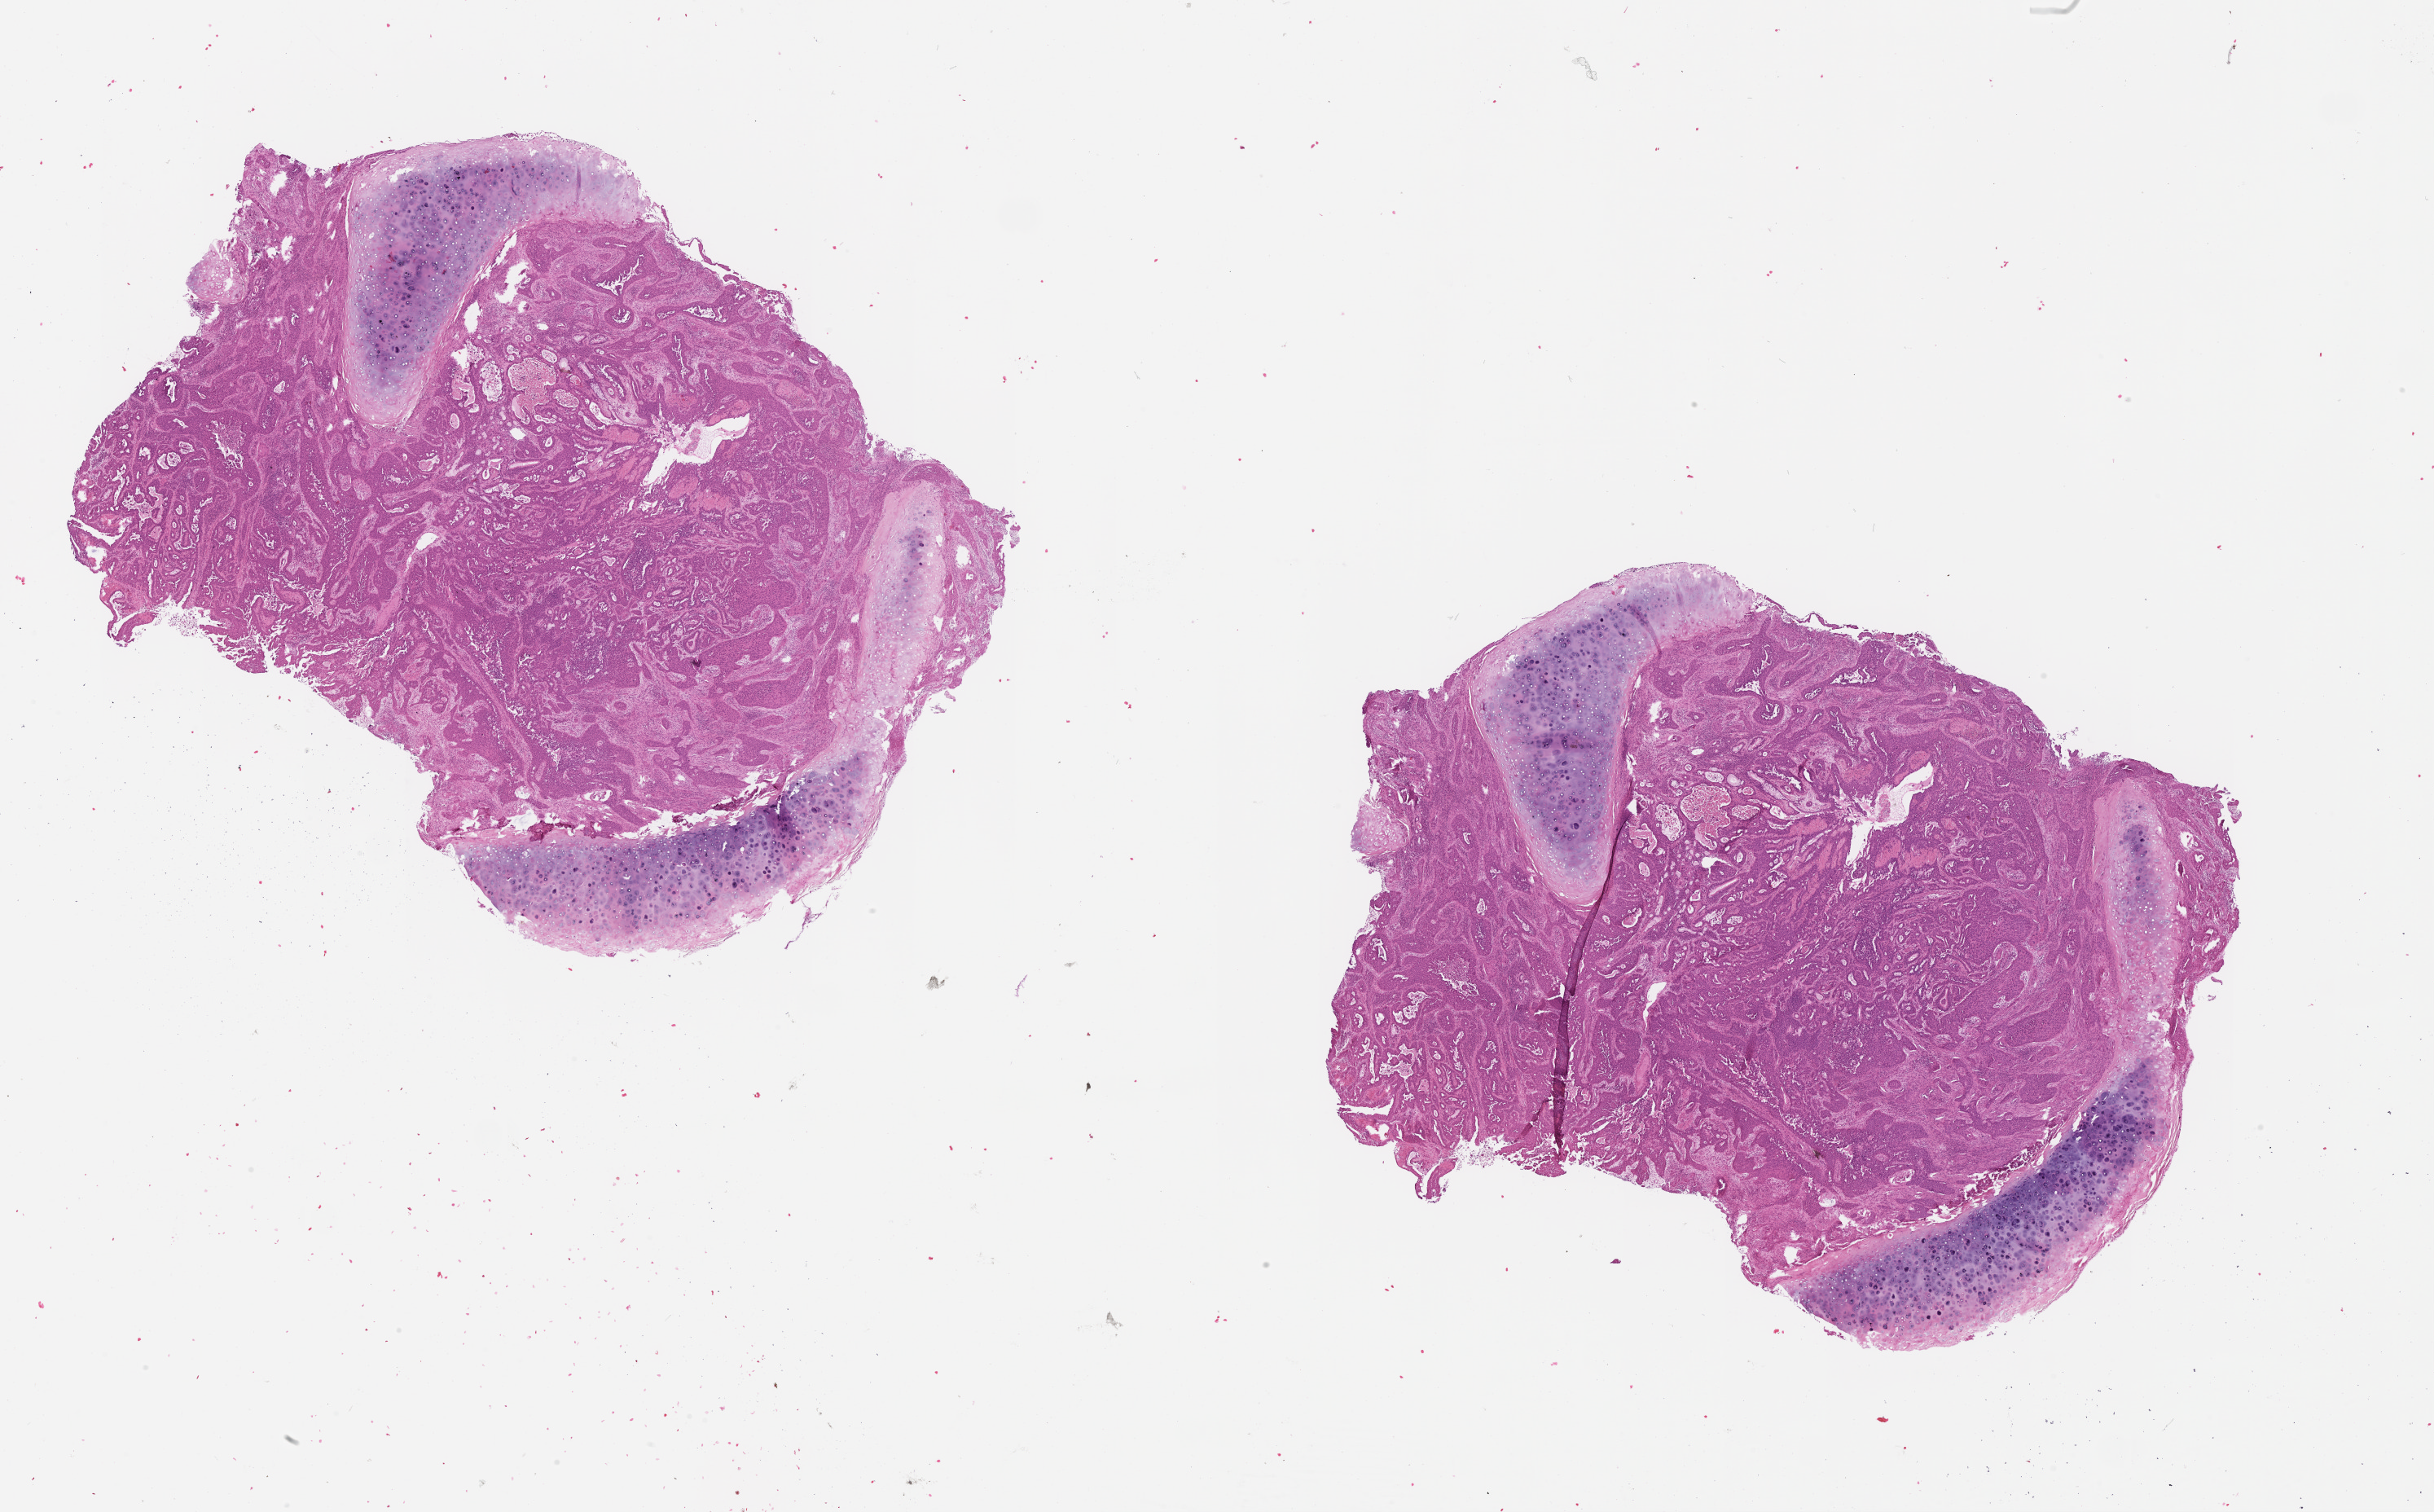
Digitized Hematoxylin and eosin (H&E) stained tissue section (whole slide) — whole scanned area (about 24.1 x 14.9 mm) shown as a low-resolution overview. Lung, tumour tissue. 55-year-old male patient.
- patient diagnosis (cohort enrolment): squamous cell carcinoma (lung)